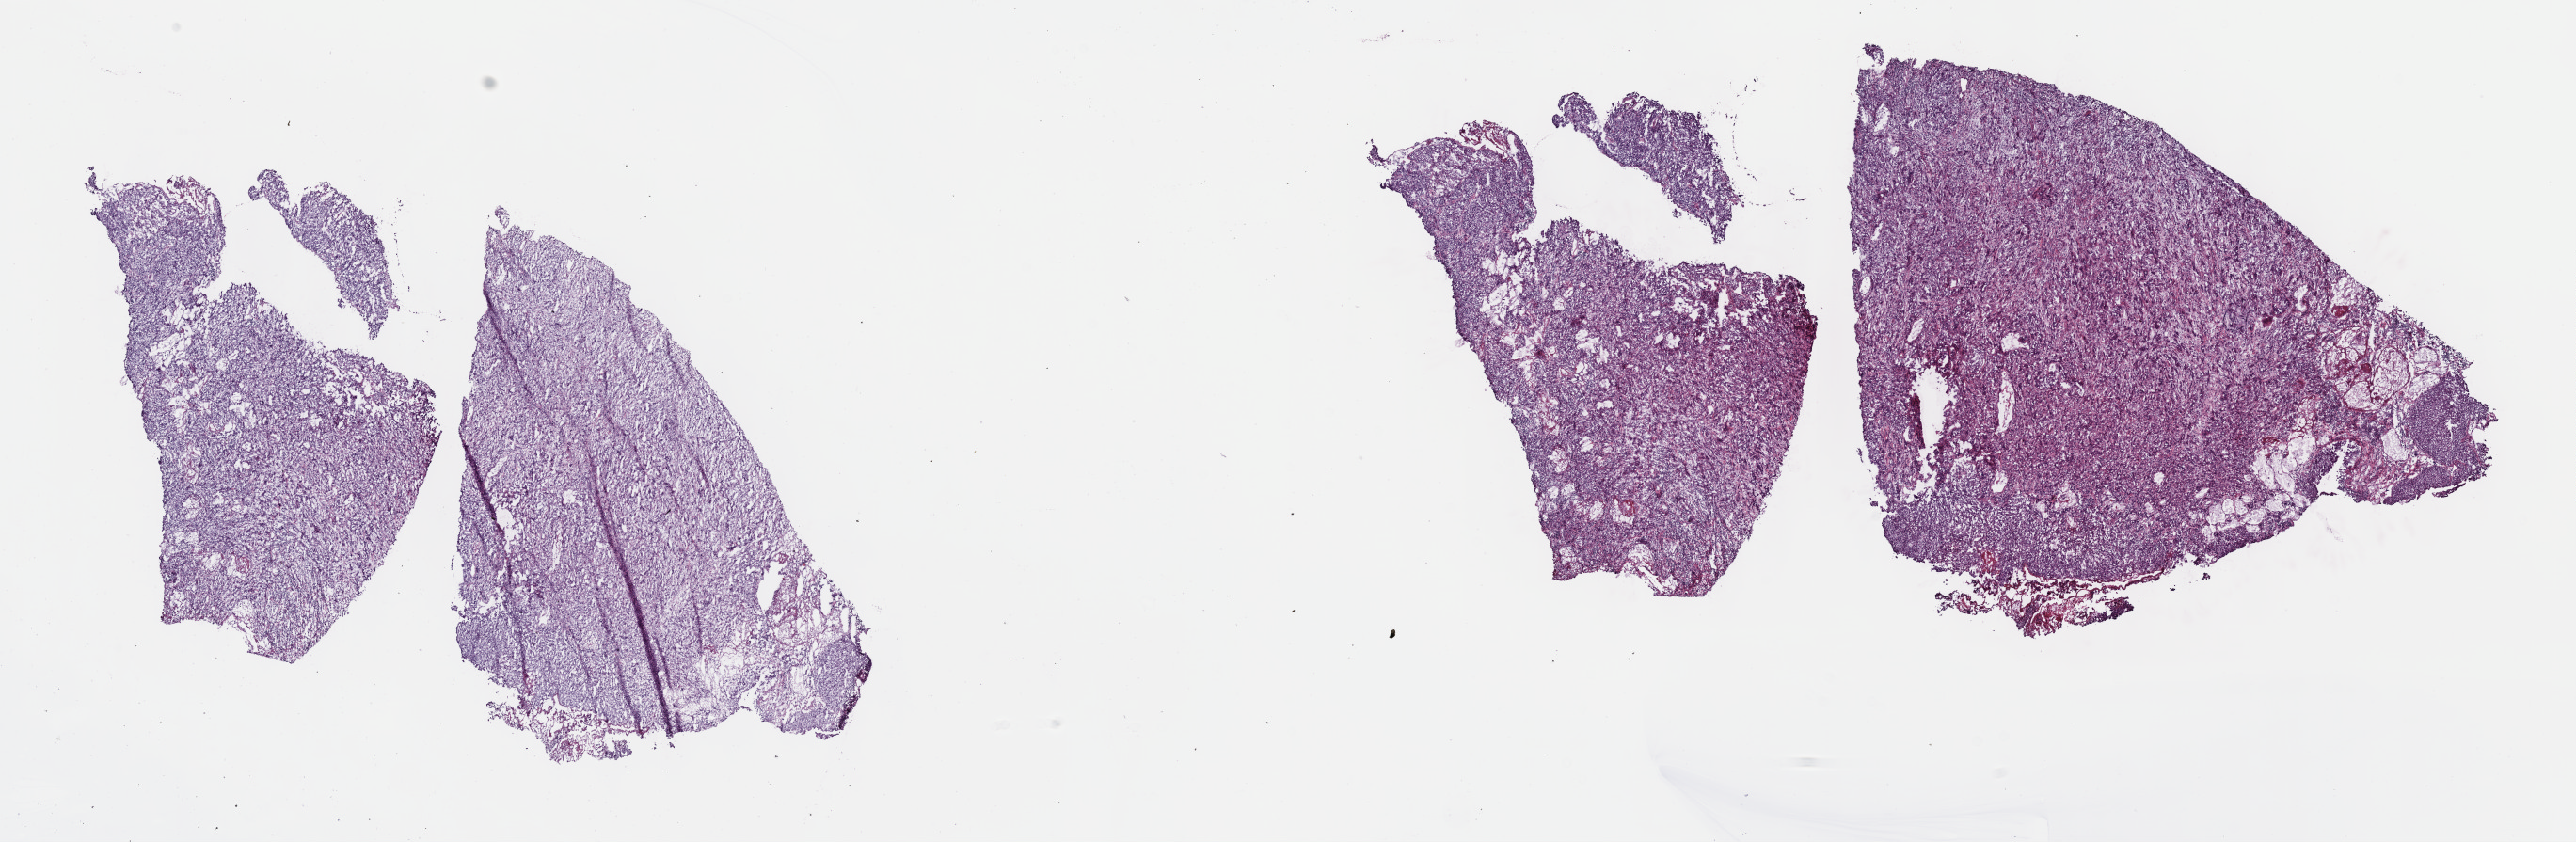
Digitized Hematoxylin and eosin (H&E) stained tissue section (whole slide), low-resolution overview of the scanned area, about 22.1 x 7.2 mm (from a 40x scan). Frozen section from the top of the tissue portion. Primary tumour sample from the bladder. Patient: male, age at initial diagnosis 47 years. Histologic grade: high grade. Pathologist review of this section (percent, as recorded): tumour cells 80%, tumour nuclei 80%, normal cells 3%, stromal cells 17%, necrosis 0%. Infiltration values recorded for this section: lymphocyte infiltration 2%, monocyte infiltration 1%, neutrophil infiltration 3%.
* histologic diagnosis: Transitional cell carcinoma (lateral wall of bladder)
* AJCC pathologic stage: III (6th edition)